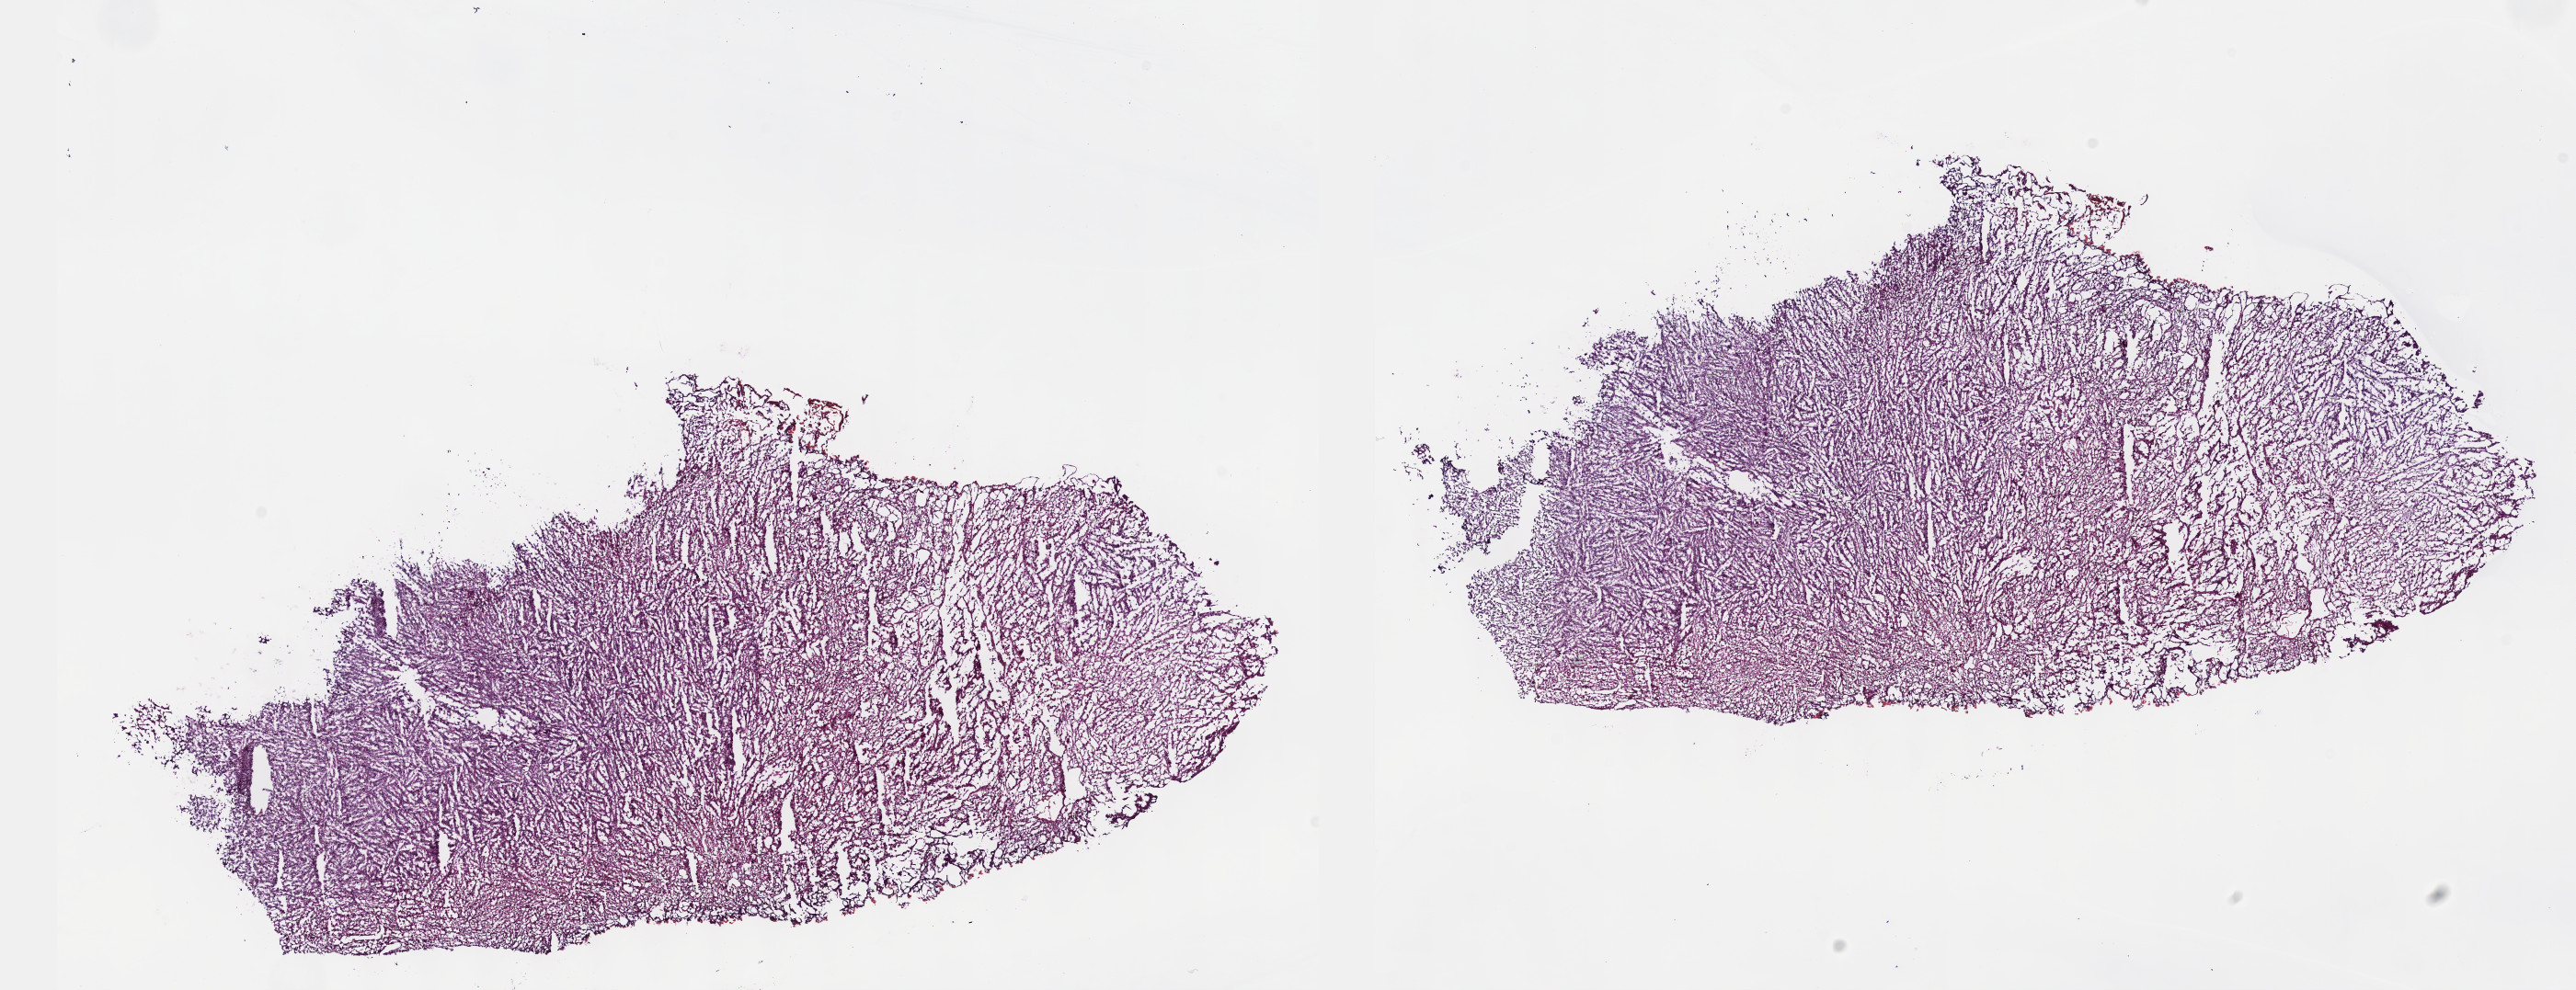
Whole-slide histology image, H&E-stained, whole scanned area (about 22.6 x 8.7 mm, slide scanned at 40x) shown as a low-resolution overview; frozen section from the top of the tissue portion; bladder, primary tumour sample. Patient: male, age at initial diagnosis 74 years. Histologic grade: high grade. Composition of this section per pathologist review: tumour cells 100%, tumour nuclei 80%, normal cells 0%, stromal cells 0%, necrosis 0%. Infiltration values recorded for this section: lymphocyte infiltration 2%, monocyte infiltration 0%, neutrophil infiltration 0%.
• AJCC pathologic stage: II (6th edition)
• TNM: T1 NX M0
• diagnosis: Transitional cell carcinoma